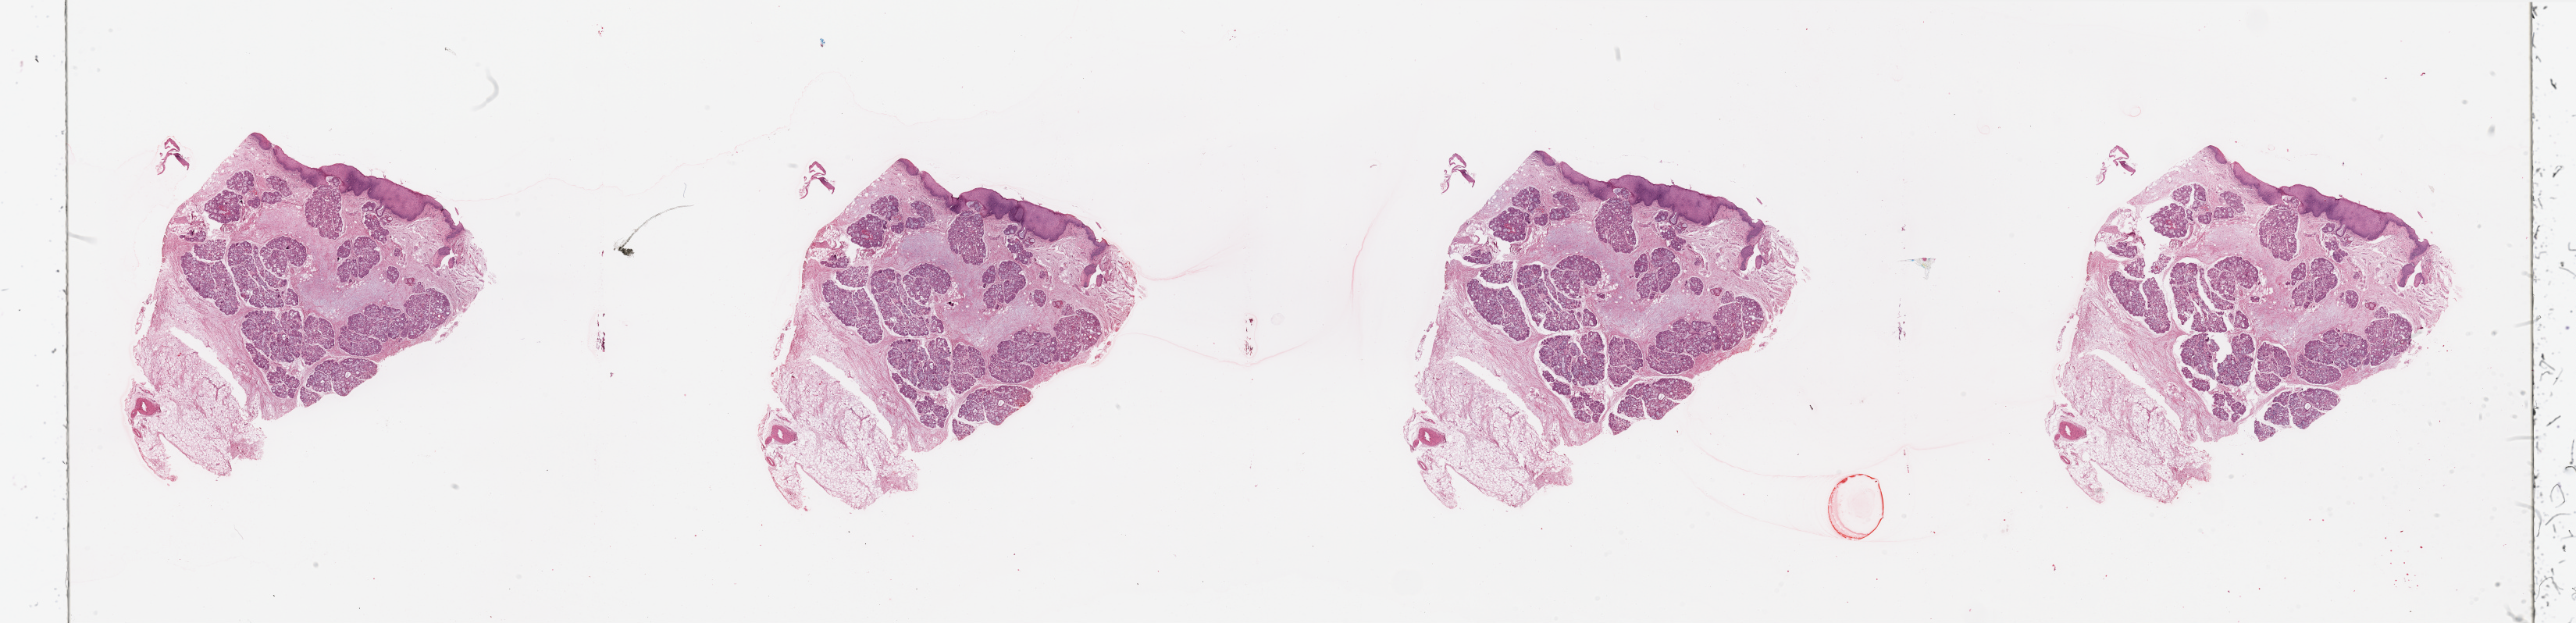
H&E whole-slide image — shown as a low-resolution overview of the whole scanned area (about 52.2 x 12.6 mm, slide scanned at 20x); normal (non-tumour) tissue sample, sampled site: larynx. 68-year-old male patient.
This section: normal (non-tumour) tissue from the same patient. Patient diagnosis: Squamous cell carcinoma, NOS.